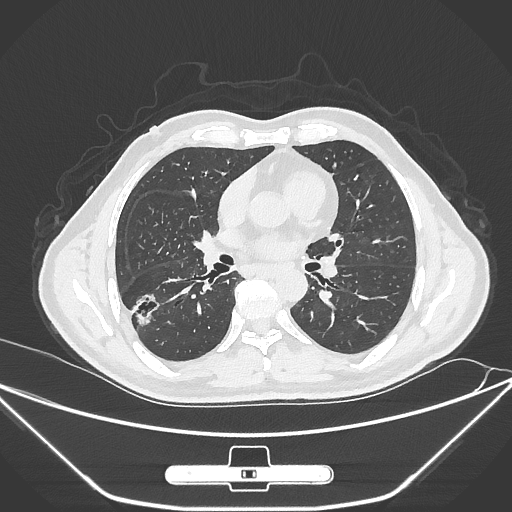
Chest CT, one axial slice; position 149 of 310 along the scan axis; reconstruction kernel IMR1,SharpPlus; 120 kVp; lung window (W 1500 / L -600 HU); 512 × 512 image matrix. Male patient, age 71 years. Case-level facts recorded for this patient, not image findings: clinical TNM (as recorded): T1c N0 M0; histopathological grade: G2.
Structures marked on this image (rectangle marked by the reading radiologist):
- lung tumour (recorded histology: adenocarcinoma): bounding box <125,281,166,329> (left, top, right, bottom; pixels)